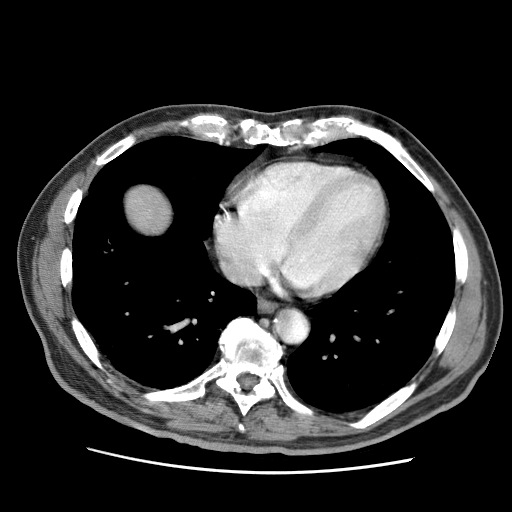
Contrast-enhanced abdominal CT (liver protocol), one axial slice; position 68 of 75 along the scan axis; 120 kVp; soft-tissue window (W 400 / L 40 HU); 512 × 512 image matrix, field of view 360 × 360 mm. From the clinical record (not read from this slice): diagnosis: hepatocellular carcinoma (patient treated with transarterial chemoembolisation; whether this scan precedes or follows treatment is not stated here); TNM stage (as recorded): Stage-IIIA; Child-Pugh class: A; tumour nodularity: multinodular.
Structures marked on this image (semi-automatically segmented with operator editing):
- liver parenchyma outside the tumour (the mass and vessels are separate outlines, so this box may not span the whole liver): box from (x=126, y=185) to (x=172, y=234) px